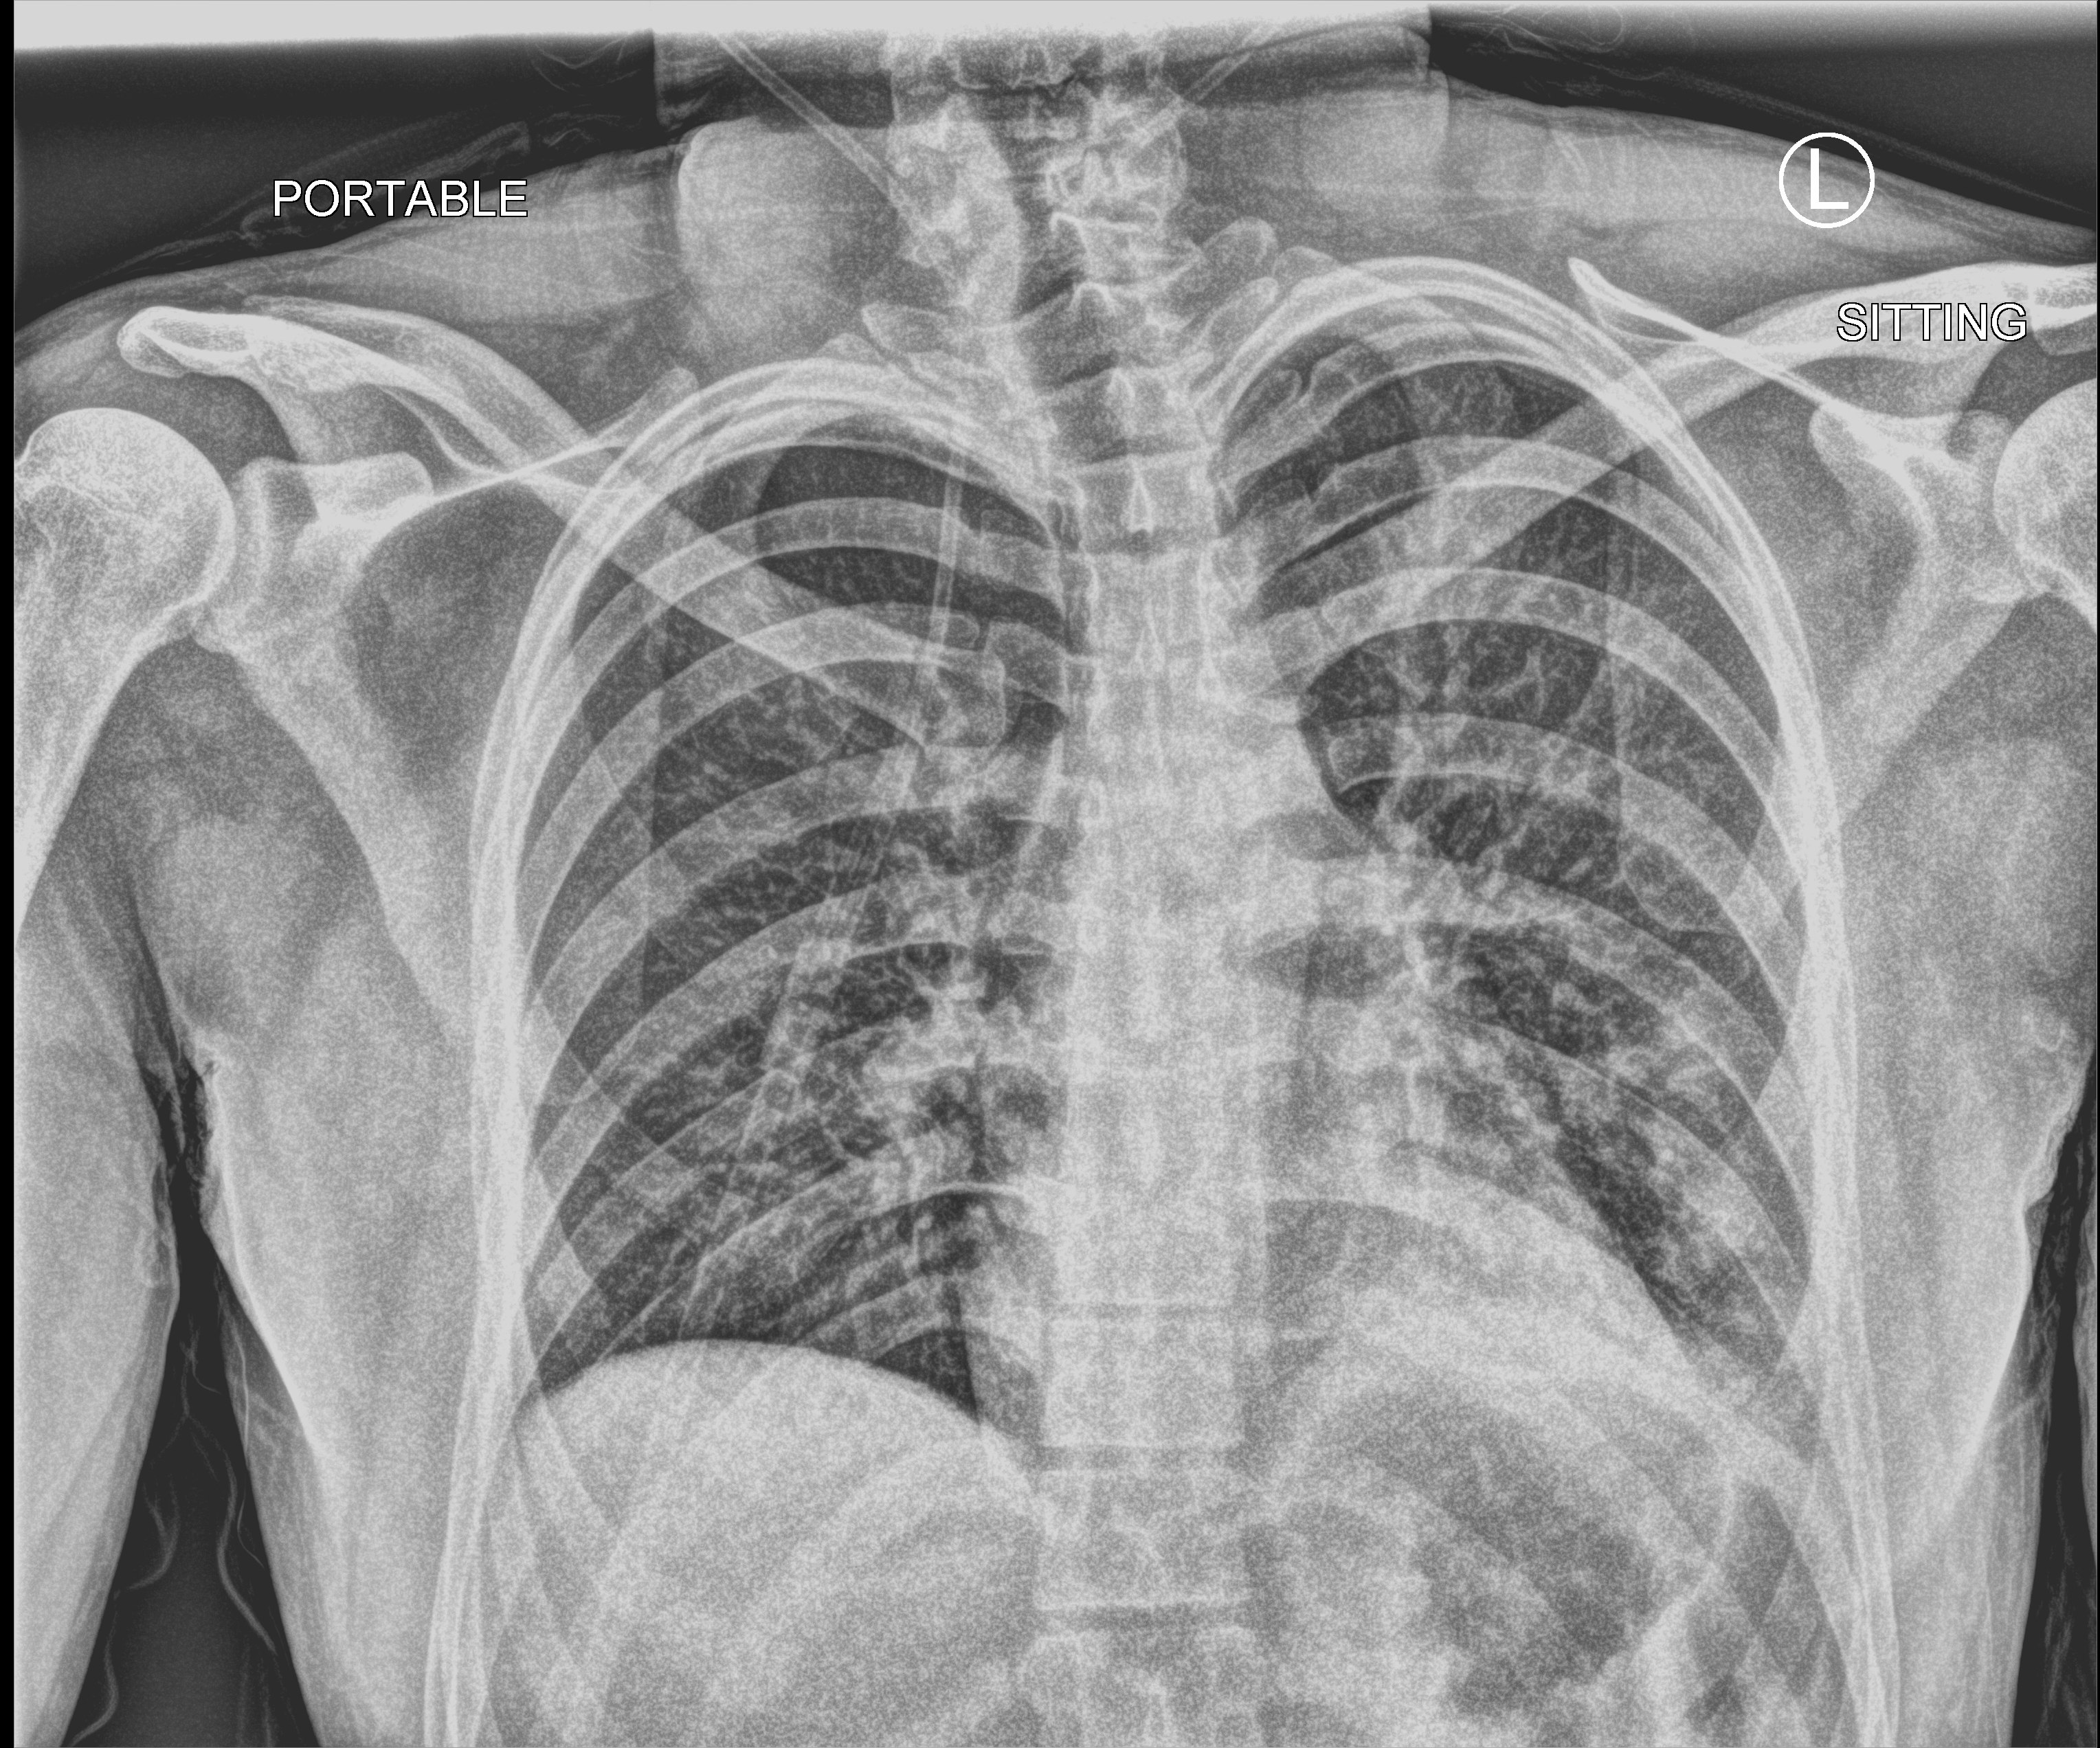
Portable chest radiograph. Patient hospitalised with COVID-19; male, aged 18–59 years.
Hospital-stay facts (about this admission, not read from this image; timing relative to this image not recorded): hypertension (admission record): no; mechanically ventilated during this hospital stay: no; COPD (admission record): no.